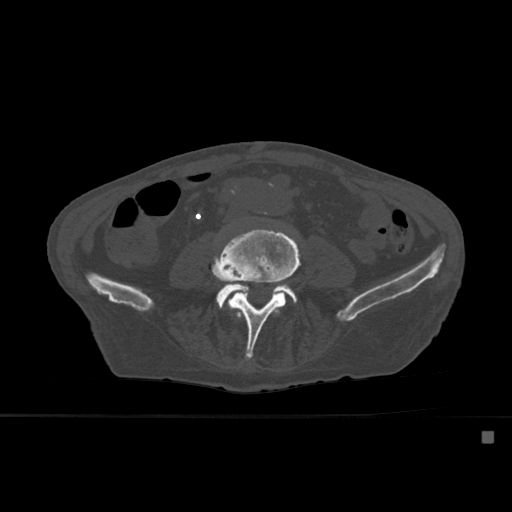
CT including the spine, one axial slice. Slice 191 of 527 in the series (ordered by position). Bone window (W 1800 / L 400 HU). 1.5 mm slice thickness. 512 × 512 image matrix, field of view 373 × 373 mm. Patient: male, 78 years. From the clinical record (not read from this slice): primary cancer: prostate.
Structures marked on this image (semi-automatic segmentation, software-assisted and operator-edited):
- L3 vertebra: bounding box [x1, y1, x2, y2] px = [232, 310, 281, 319]
- L4 vertebra: [212, 228, 300, 360]
- L5 vertebra: [216, 283, 297, 308]